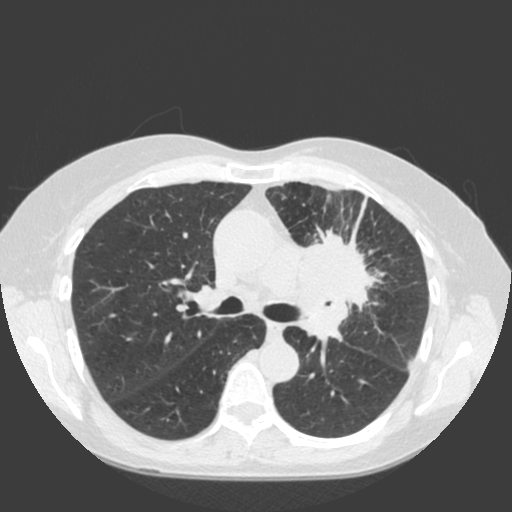
Chest CT (low-dose screening protocol), one axial image; baseline annual screen; lung window (W 1500 / L -600 HU); 2 mm slice thickness; standard (soft-tissue) reconstruction kernel (C); slice 65 of 184 in the series; 512 × 512 image matrix. Female, age 66 years at enrolment.
• Expert-annotated lung lesion, bounding box [x1, y1, x2, y2] px = [279, 215, 400, 324].
• Reader record for this screening exam (exam-level; its link to the box is not recorded): non-calcified nodule or mass ≥4 mm, left upper lobe, 61 × 45 mm, spiculated (stellate) margins, soft tissue attenuation.
• Official screen result: positive, change unspecified: nodule(s) >= 4 mm or enlarging nodule(s), mass(es), or other non-specific abnormalities suspicious for lung cancer.
• Later outcome: lung cancer diagnosed 19 days after this screen — squamous cell carcinoma, keratinizing, NOS, left upper lobe, left hilum, mediastinum, left main stem bronchus, other location, poorly differentiated (G3), stage IIIB (AJCC 6th edition), 60 mm at pathology.